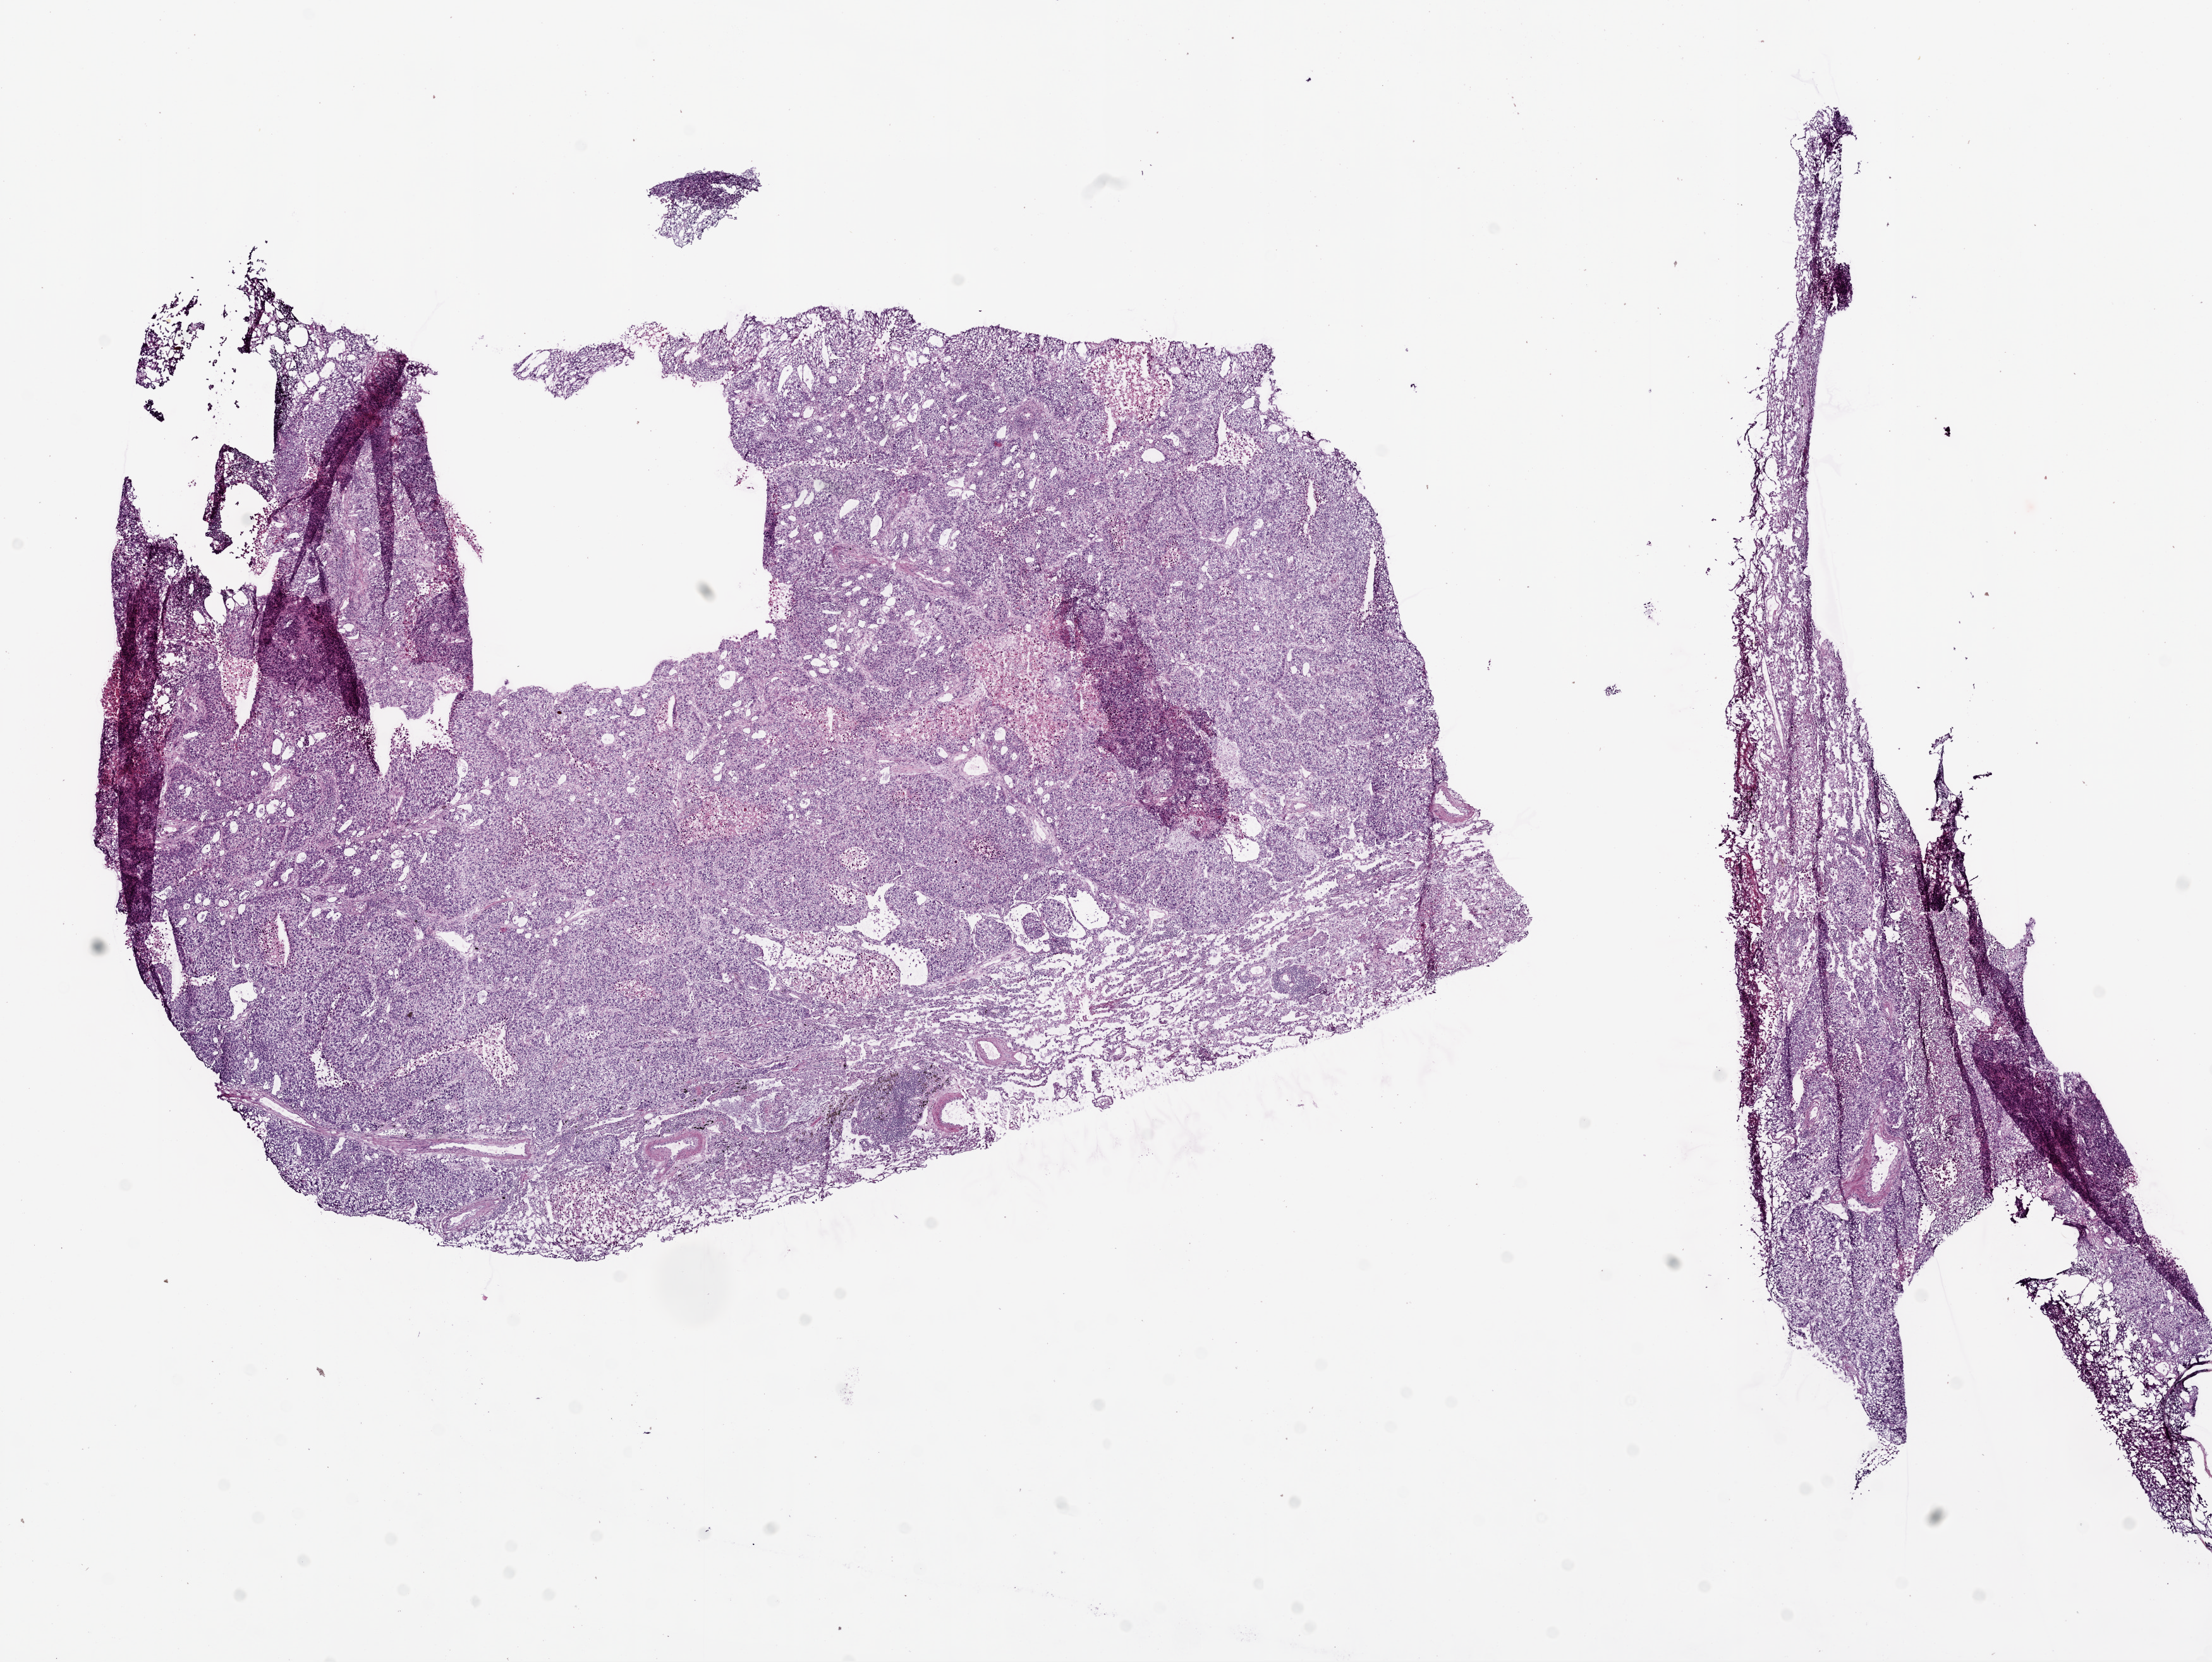
Digitized Hematoxylin and eosin (H&E) stained tissue section (whole slide) — shown as a low-resolution overview of the whole scanned area (about 14.0 x 10.5 mm, acquisition: 20x scan). Frozen section from the bottom of the tissue portion. Primary tumour sample from the lung. Male, age 68 years at initial diagnosis. Pathologist review of this section (percent, as recorded): tumour cells 80%, tumour nuclei 85%, normal cells 5%, stromal cells 5%, necrosis 10%.
AJCC pathologic stage: IB (5th edition). Diagnosis: Squamous cell carcinoma, NOS.